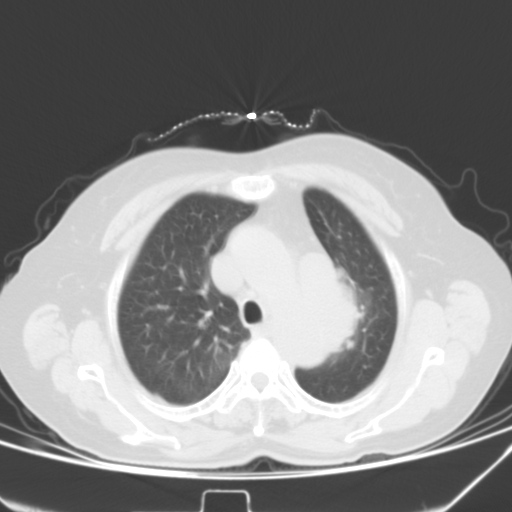
Chest CT, one axial slice; position 33 of 42 along the scan axis; lung window (W 1500 / L -600 HU); 5 mm slice thickness; 512 × 512 image matrix, field of view 331 × 331 mm. Female patient, age 59 years. Case-level facts recorded for this patient, not image findings: clinical TNM (as recorded): T3 N1 M0.
Structures marked on this image (bounding box drawn by a radiologist):
- lung tumour (recorded histology: small cell carcinoma): box from (x=335, y=277) to (x=372, y=365) px